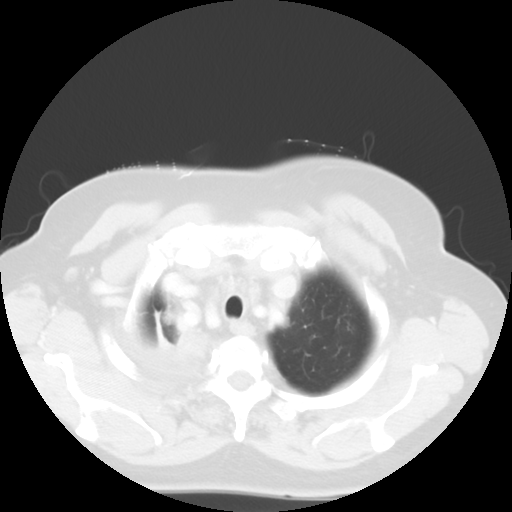
Chest CT, one axial slice; position 47 of 52 along the scan axis; reconstruction kernel STANDARD; 120 kVp; lung window (W 1500 / L -600 HU); 5 mm slice thickness; 512 × 512 image matrix, field of view 333 × 333 mm. Patient: female, 81 years. Case-level facts recorded for this patient, not image findings: clinical TNM (as recorded): T4 N3 M1b.
Structures marked on this image (bounding box drawn by a radiologist):
- lung tumour (recorded histology: adenocarcinoma): bounding box (x1, y1, x2, y2) in pixels: (144, 309, 212, 377)